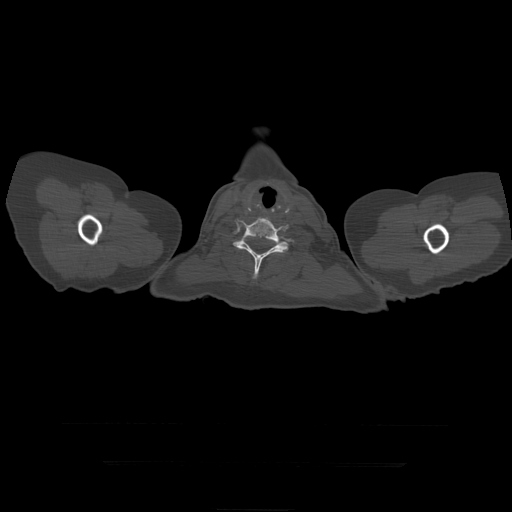
CT including the spine, one axial slice. Position 398 of 399 along the scan axis. Reconstruction kernel STANDARD. 120 kVp. Bone window (W 1800 / L 400 HU). 1.25 mm slice thickness. 512 × 512 image matrix. Patient age 41 years. Case-level facts recorded for this patient, not image findings: primary cancer: breast.
Annotated regions visible in this slice (semi-automatic segmentation, software-assisted and operator-edited):
- T1 vertebra: bounding box <233,236,249,250> (left, top, right, bottom; pixels)